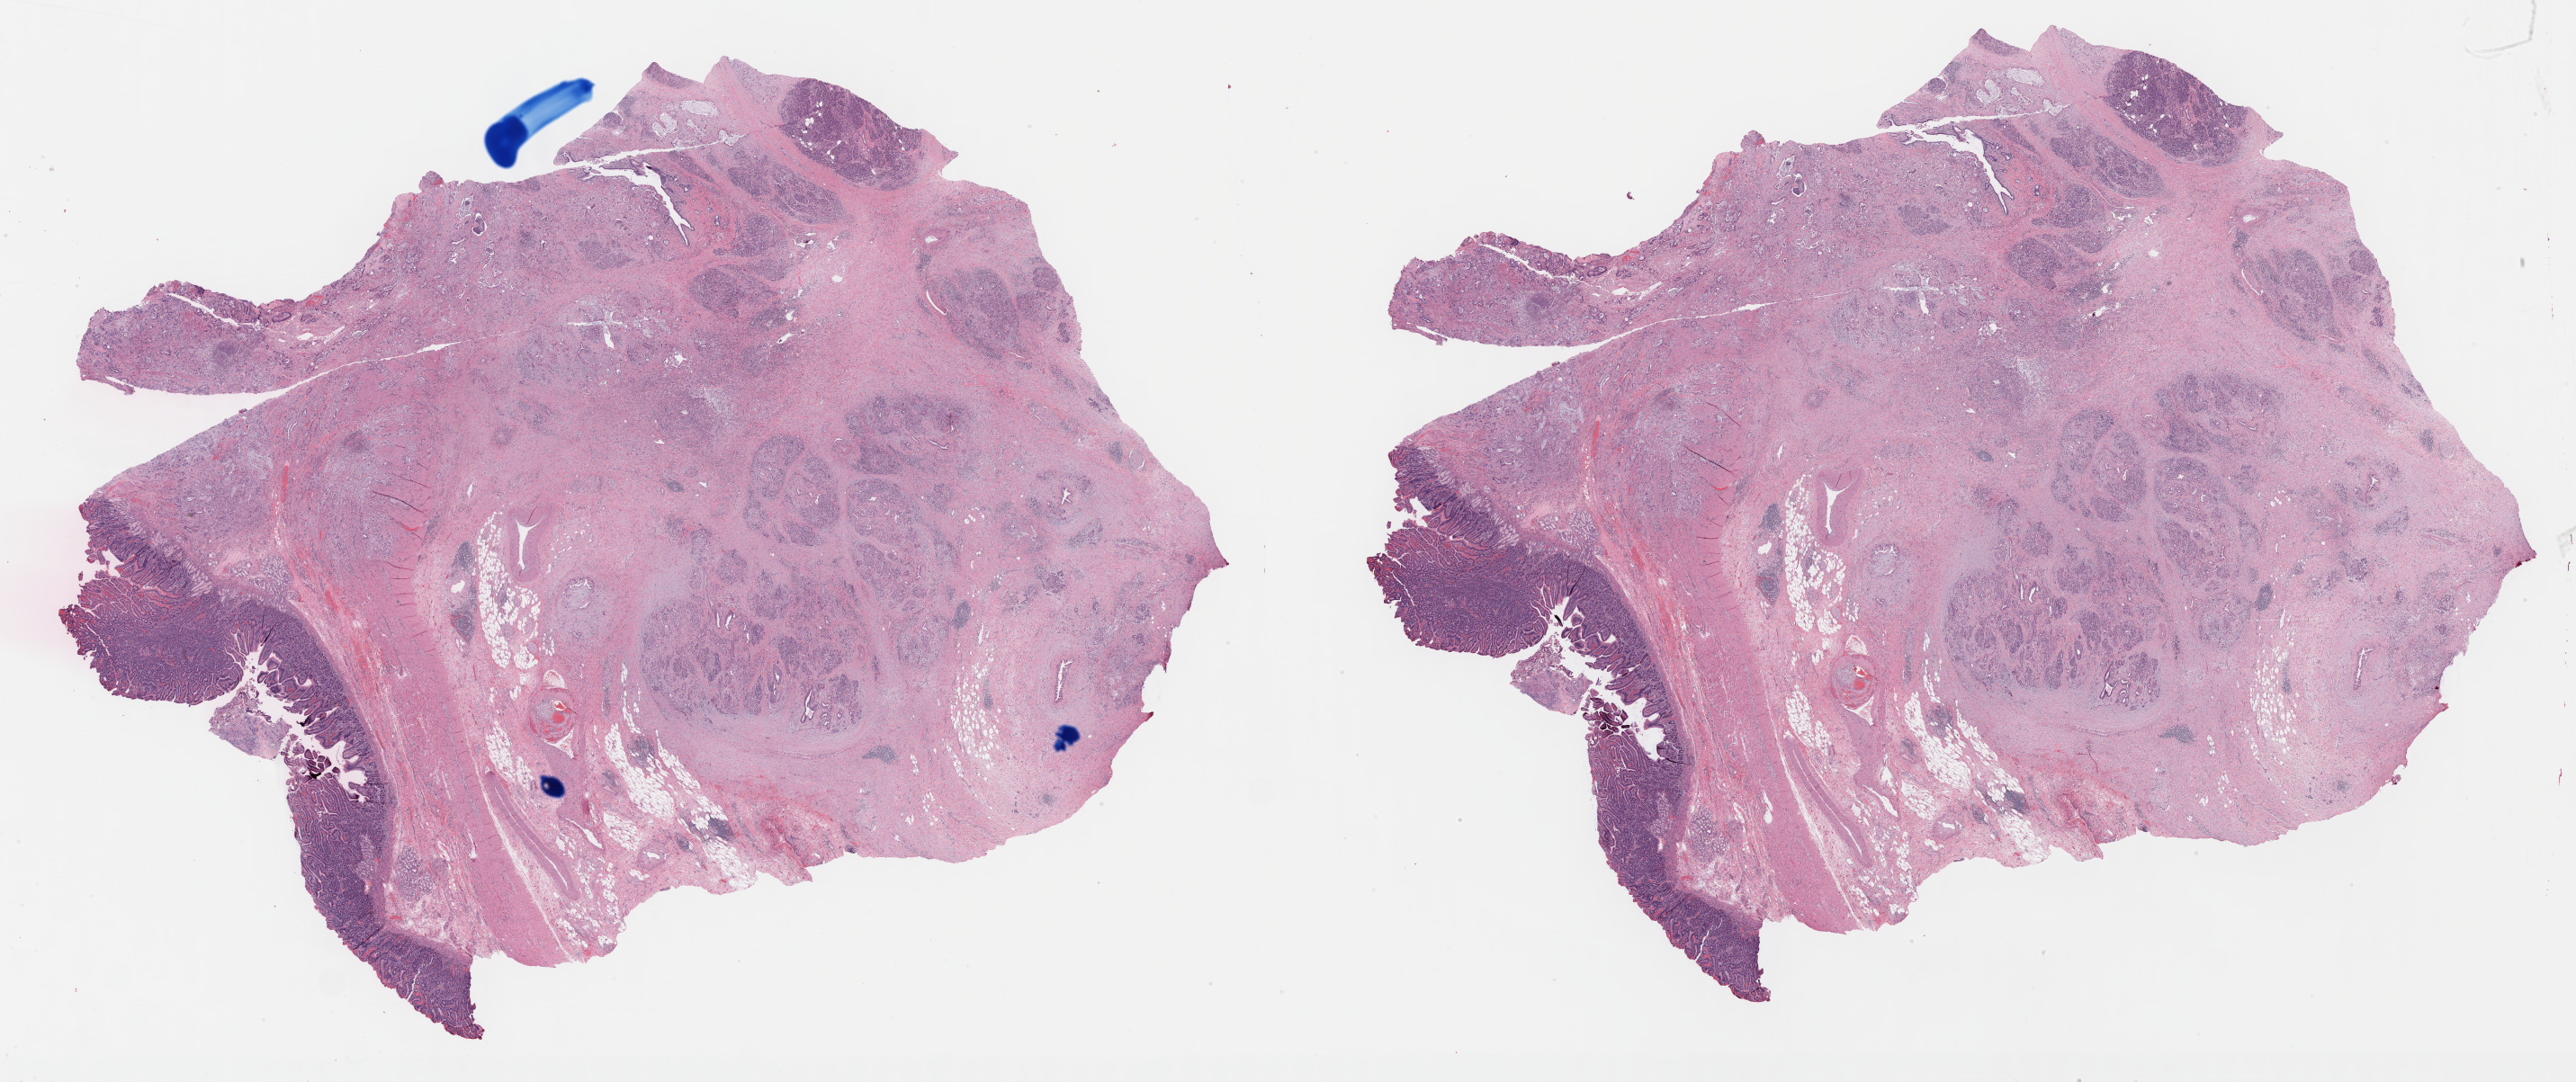
Whole-slide histology image, Hematoxylin and eosin (H&E) stained, low-resolution overview of the scanned area, about 46.3 x 19.5 mm (from a 40x scan); FFPE section; sample: primary tumour, pancreas. Patient: male, age at initial diagnosis 49 years. Histologic grade: G2 (moderately differentiated).
Lymph nodes positive (case pathology): 3 of 15 examined. AJCC pathologic stage: IIB. Pathologic diagnosis: Infiltrating duct carcinoma, NOS.